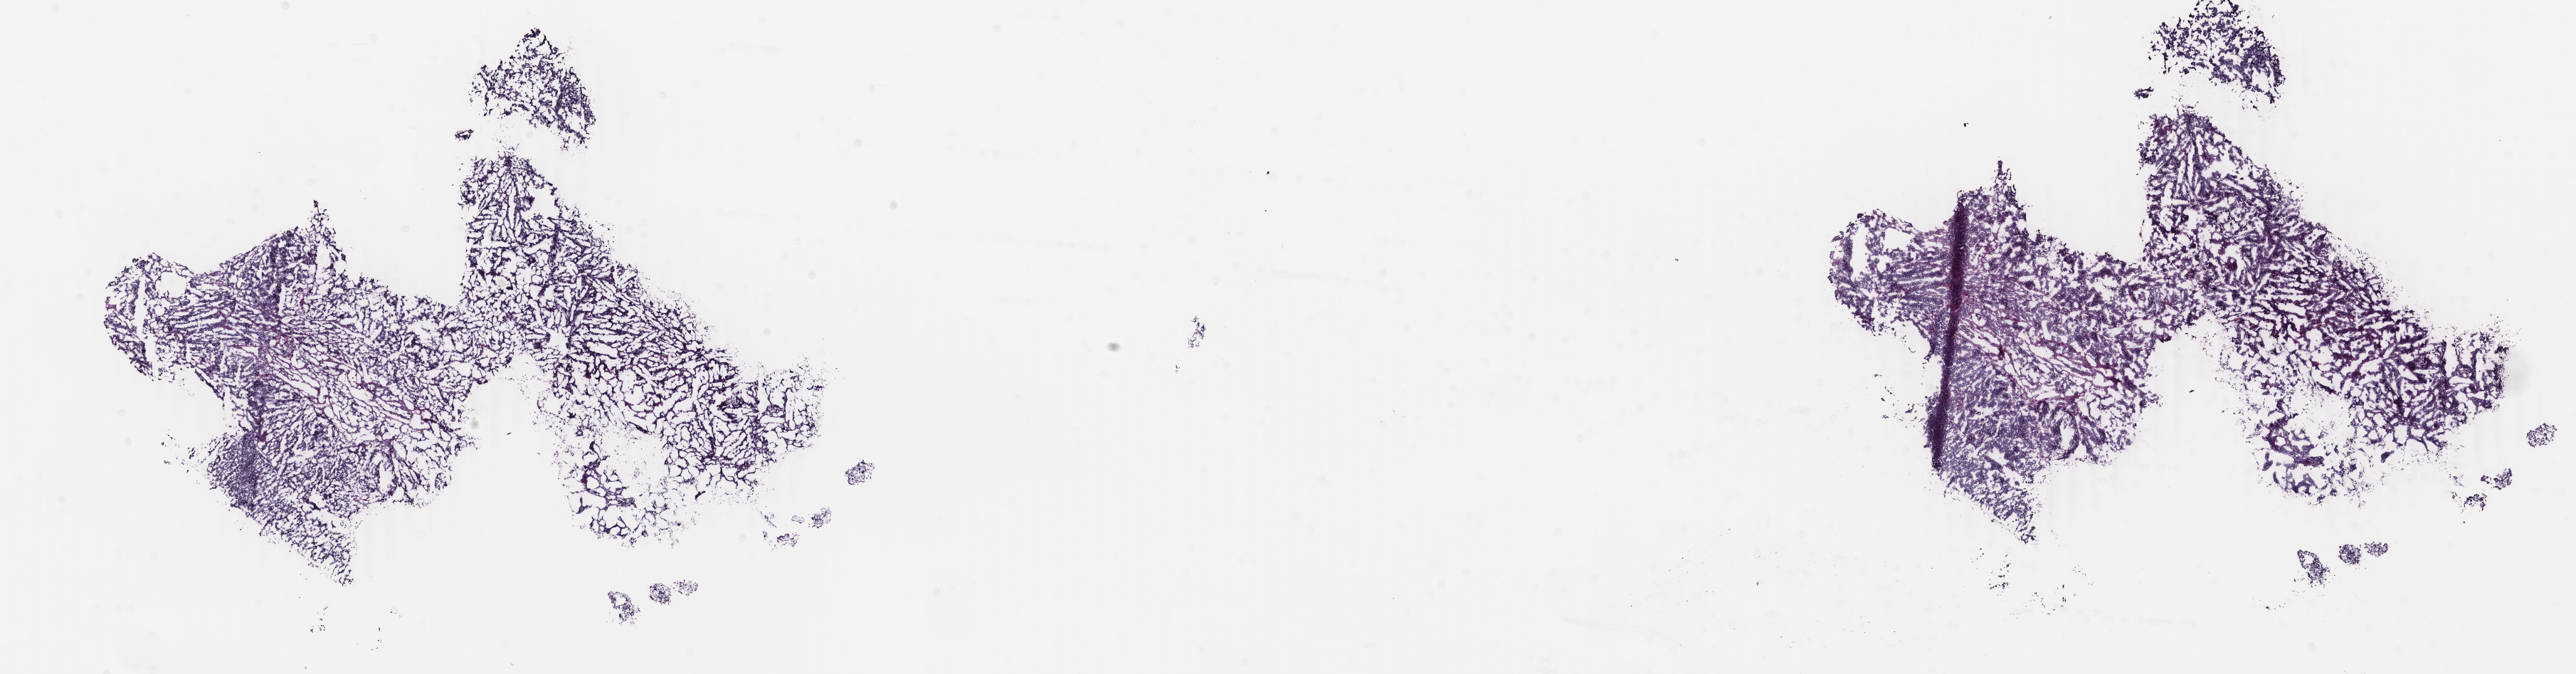
Digitized H&E tissue section (whole slide) — shown as a low-resolution overview of the whole scanned area (about 28.8 x 7.5 mm, slide scanned at 40x). Frozen section from the bottom of the tissue portion. Uterus, primary tumour sample. Patient: female, age at initial diagnosis 64 years. Histologic grade: G3 (poorly differentiated). Pathologist review of this section (percent, as recorded): tumour cells 90%, tumour nuclei 90%, normal cells 0%, stromal cells 10%, necrosis 0%. Inflammatory infiltration, as recorded: lymphocyte infiltration 0%, monocyte infiltration 0%, neutrophil infiltration 0%.
FIGO stage: IB. Diagnosis: Endometrioid adenocarcinoma, NOS (endometrium).